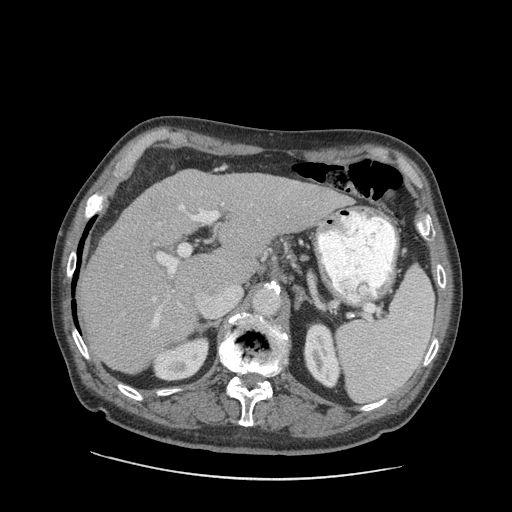
Contrast-enhanced abdominal CT (liver protocol), one axial slice; position 56 of 89 along the scan axis; reconstruction kernel STANDARD; 140 kVp; soft-tissue window (W 400 / L 40 HU); 512 × 512 image matrix, field of view 420 × 420 mm. Case-level facts recorded for this patient, not image findings: diagnosis: hepatocellular carcinoma (patient treated with transarterial chemoembolisation; whether this scan precedes or follows treatment is not stated here); TNM stage (as recorded): Stage-I; Child-Pugh class: A; tumour differentiation: moderately differentiated; tumour nodularity: uninodular.
Structures marked on this image (semi-automatic segmentation, software-assisted and operator-edited):
- liver parenchyma outside the tumour (the mass and vessels are separate outlines, so this box may not span the whole liver): bounding box [x1, y1, x2, y2] px = [78, 170, 348, 374]
- liver vessels: [120, 182, 305, 330]